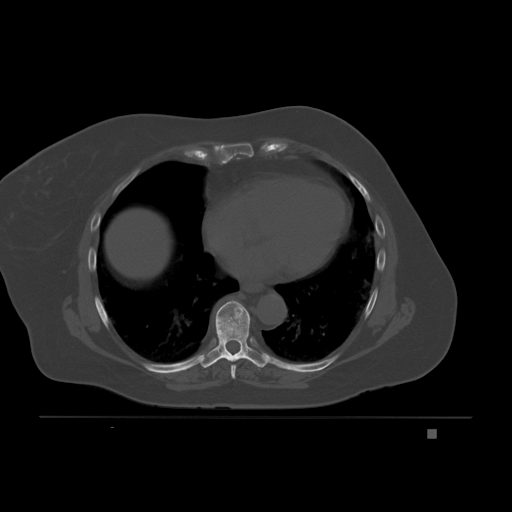
CT including the spine, one axial slice; position 120 of 221 along the scan axis; bone window (W 1800 / L 400 HU); 3 mm slice thickness; 512 × 512 image matrix, field of view 474 × 474 mm. Patient: female, 63 years. From the clinical record (not read from this slice): primary cancer: breast.
Structures marked on this image (semi-automatically segmented with operator editing):
- T7 vertebra: bounding box [x1, y1, x2, y2] px = [231, 364, 237, 379]
- T8 vertebra: [200, 300, 268, 368]